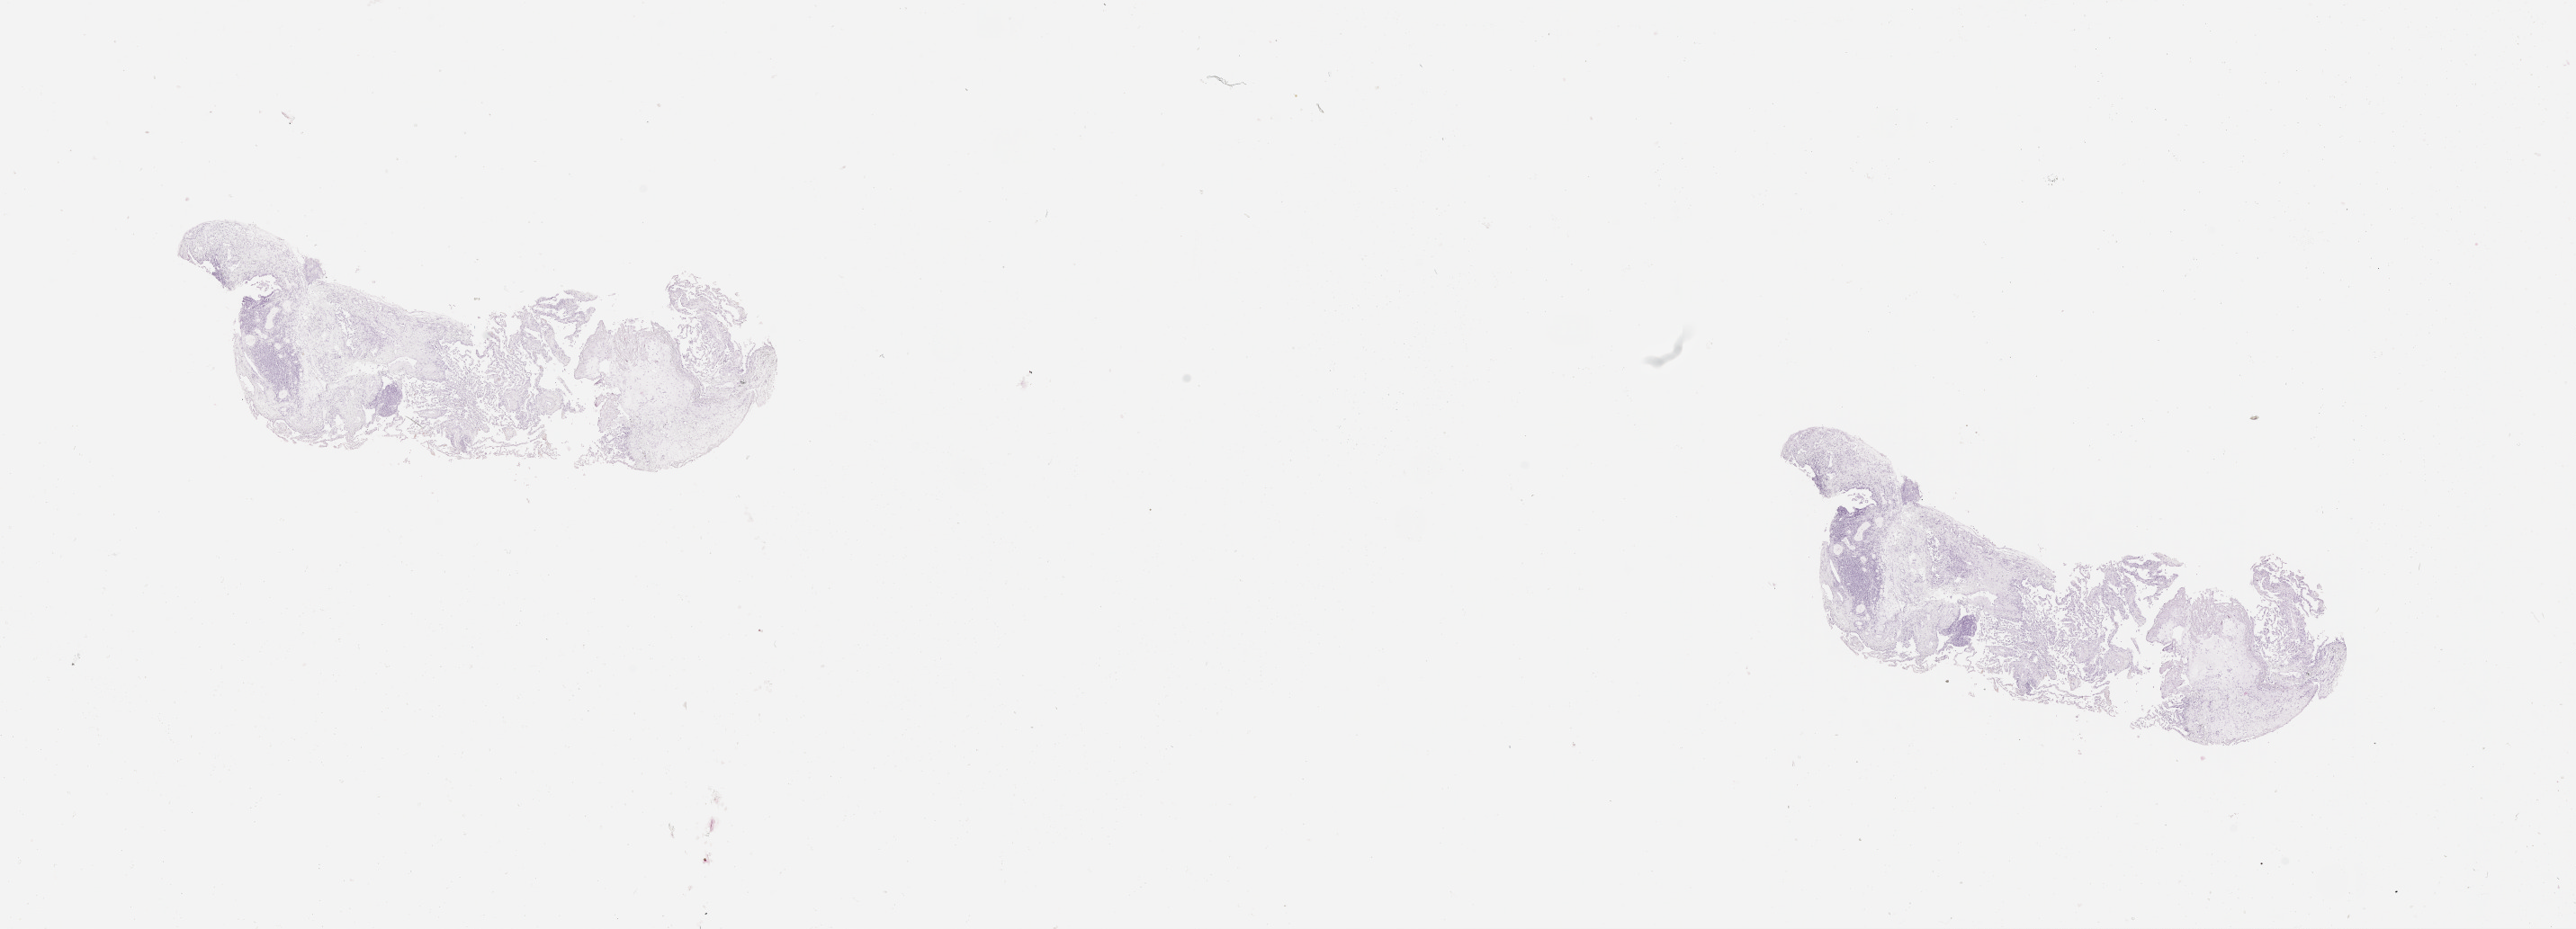
Whole-slide histology image, H&E, shown as a low-resolution overview of the whole scanned area (about 23.1 x 8.3 mm, slide scanned at 20x), lung, normal (non-tumour) tissue. Male, 66 y/o.
• this section: normal (non-tumour) tissue from the same patient
• patient diagnosis (cohort enrolment): squamous cell carcinoma (lung)